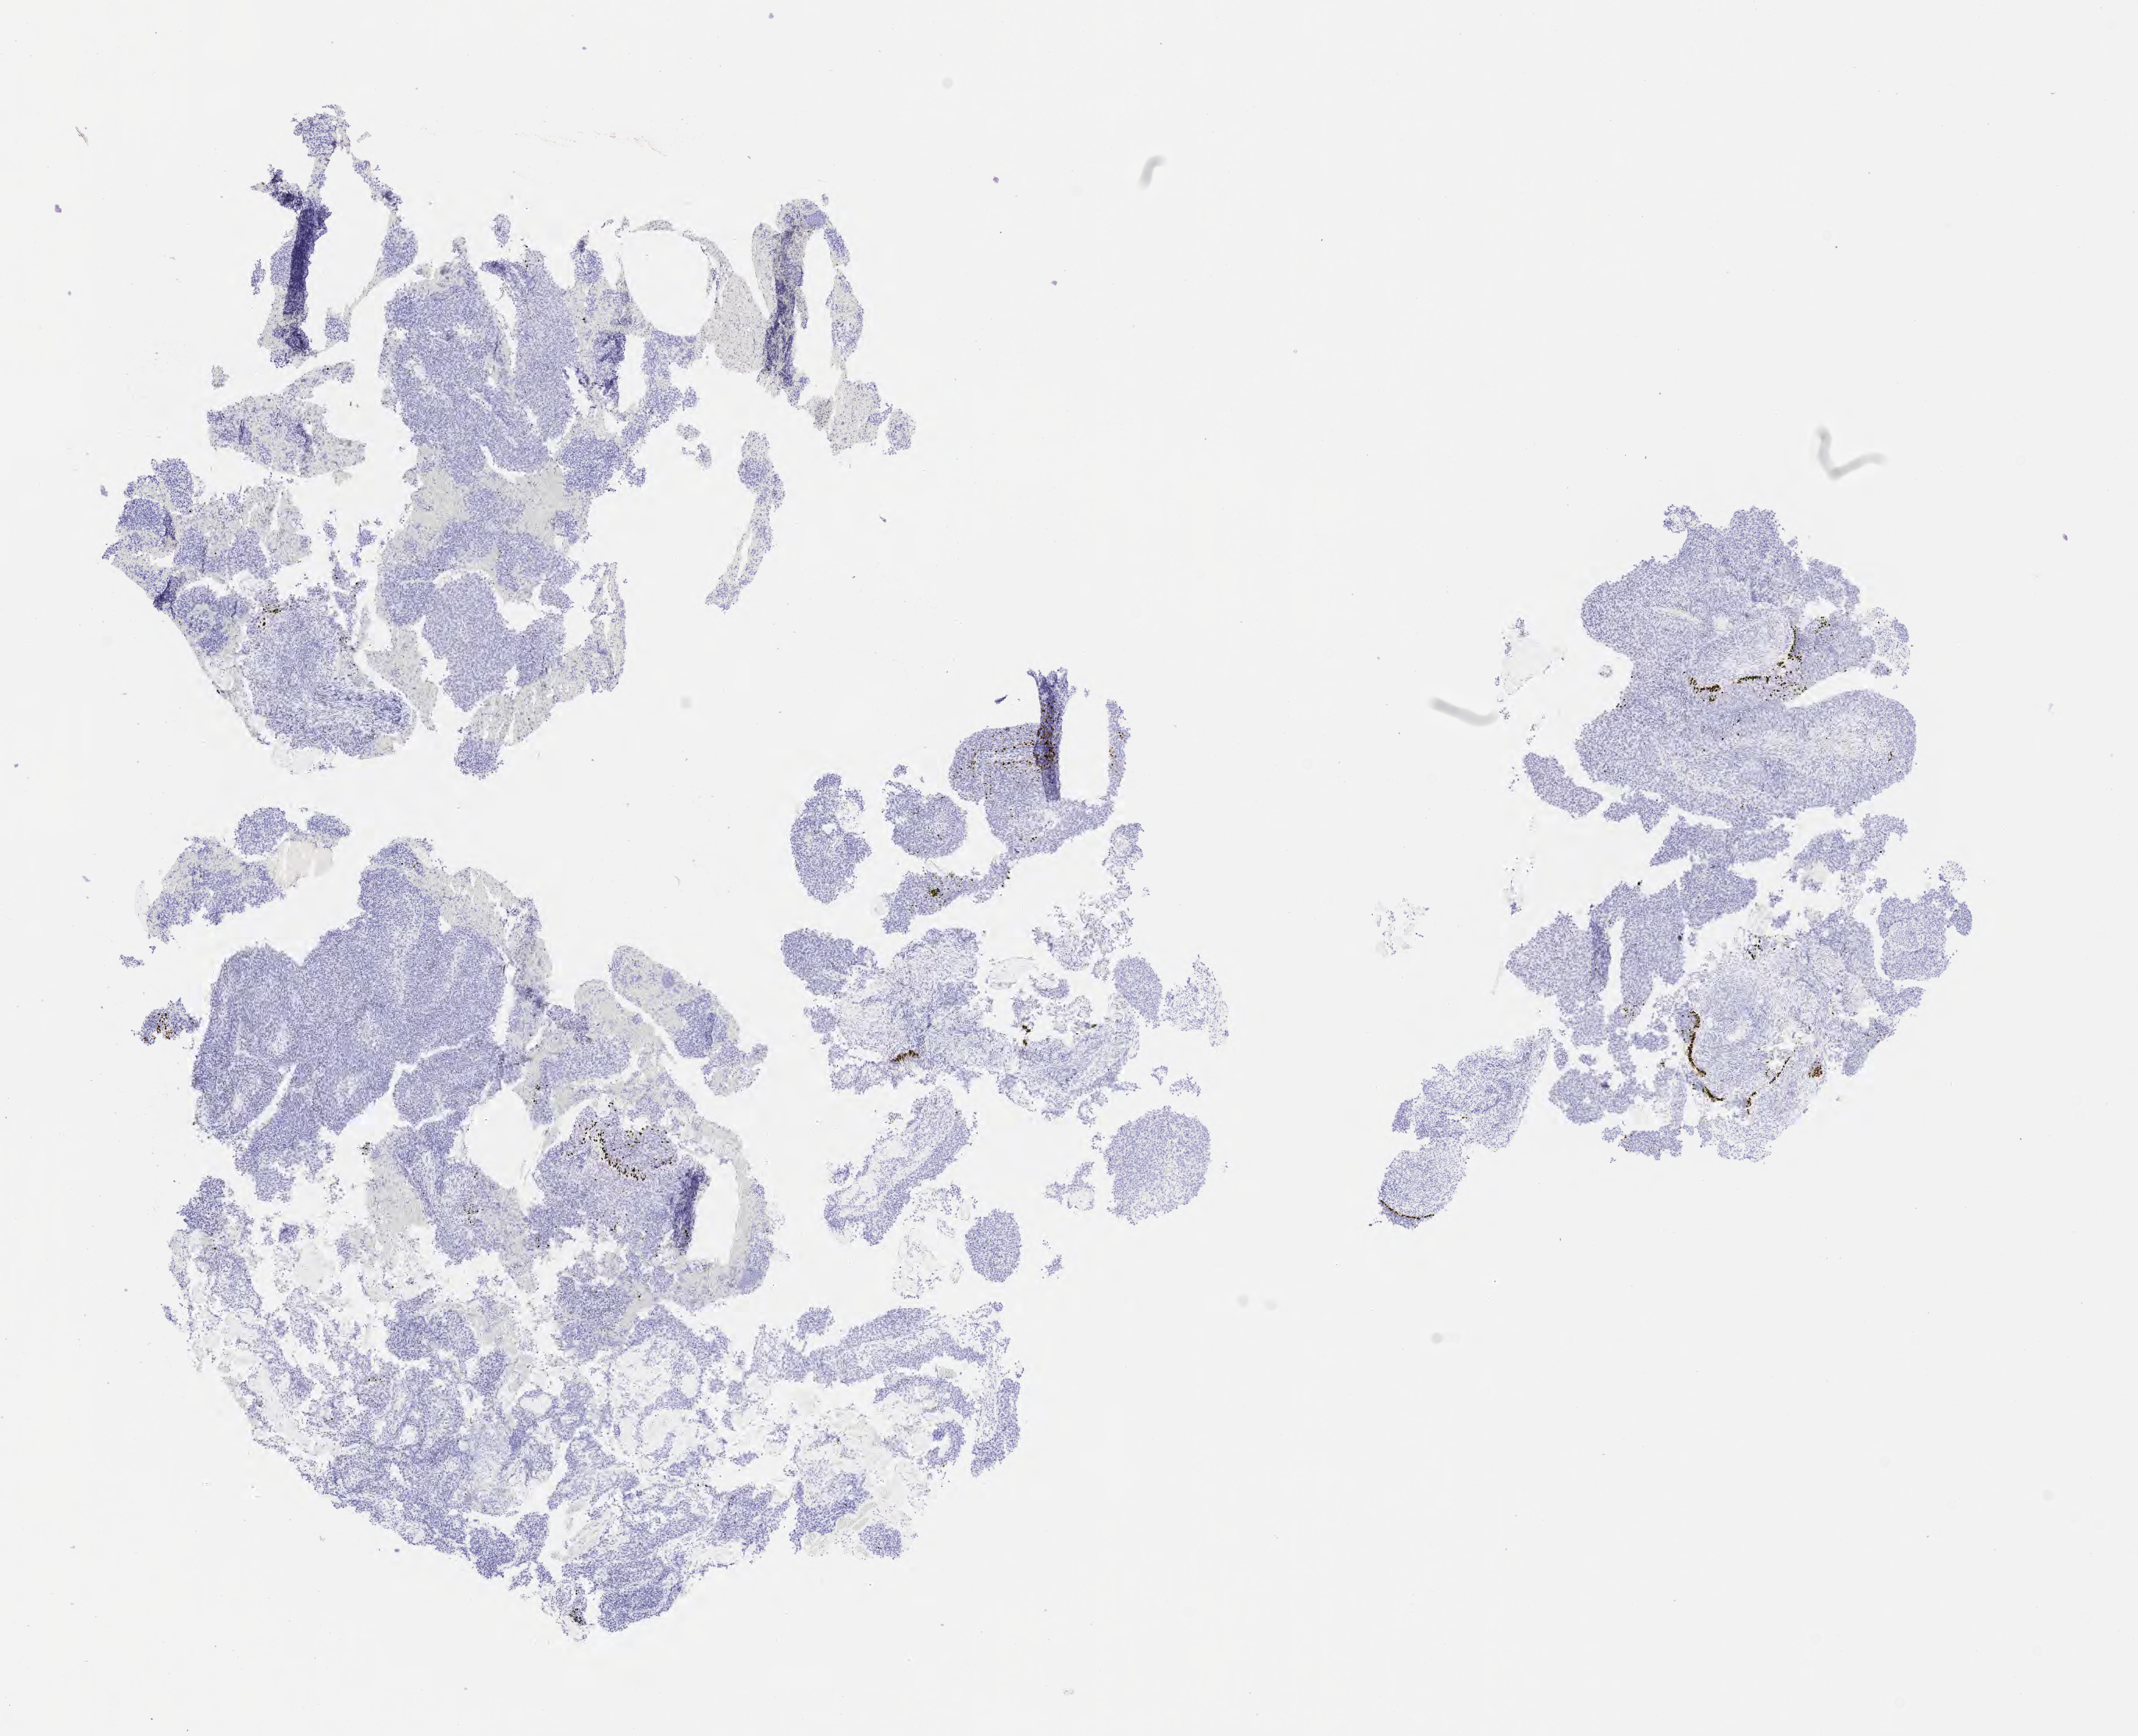
IHC for p40, whole-slide image, low-resolution overview of the scanned area, about 11.1 x 9.0 mm. Tumor tissue. Anatomic site: cervix. Female patient, age 44 years.
Diagnosis: Squamous cell carcinoma, large cell, nonkeratinizing, NOS.